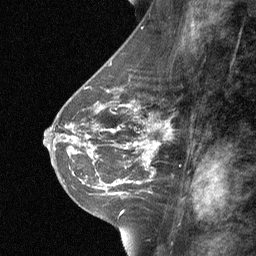
Breast MRI (dynamic contrast-enhanced), one sagittal slice; dynamic contrast-enhanced study with each time point stored as its own series, time point 2 of 3 at this slice position (early post-contrast, ordered by acquisition time); 1.5 T; TE 4.8 ms, TR 27 ms; 2 mm slice thickness; 256 × 256 image matrix, field of view 180 × 180 mm. Female patient, age 42 years. From the clinical record (not read from this slice): setting: breast cancer imaged before/during neoadjuvant chemotherapy; receptor status: triple-negative.
Annotated regions visible in this slice (semi-automatic segmentation, software-assisted and operator-edited):
- analysis volume of interest (the breast-tissue region the enhancement analysis was run in; not a lesion): box from (x=99, y=117) to (x=174, y=187) px
- tumour enhancement mask (voxels above the 90 % enhancement threshold inside the analysis volume of interest): (x=122, y=121)–(x=169, y=183)